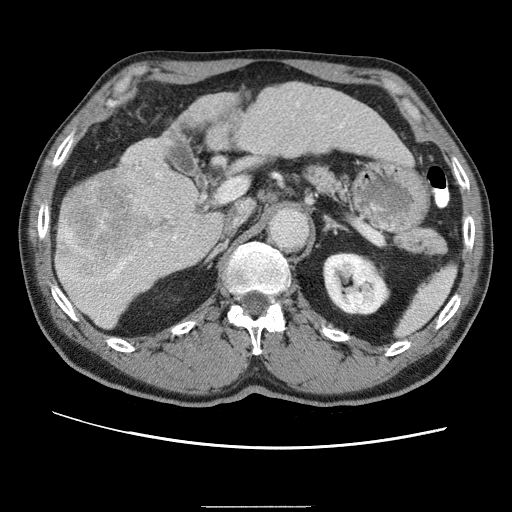
Contrast-enhanced abdominal CT (liver protocol), one axial slice. Position 27 of 75 along the scan axis. Reconstruction kernel STANDARD. One of 2 acquisitions stored at this slice position. Soft-tissue window (W 400 / L 40 HU). 2.5 mm slice thickness. 512 × 512 image matrix, field of view 360 × 360 mm. From the clinical record (not read from this slice): diagnosis: hepatocellular carcinoma (patient treated with transarterial chemoembolisation; whether this scan precedes or follows treatment is not stated here); TNM stage (as recorded): Stage-II; Child-Pugh class: A; tumour differentiation: well differentiated; tumour size: 2 cm.
Outlined on this slice (semi-automatically segmented with operator editing):
- liver parenchyma outside the tumour (the mass and vessels are separate outlines, so this box may not span the whole liver): bounding box (x1, y1, x2, y2) in pixels: (56, 84, 404, 326)
- mass: (57, 200, 137, 273)
- liver vessels: (60, 116, 299, 277)